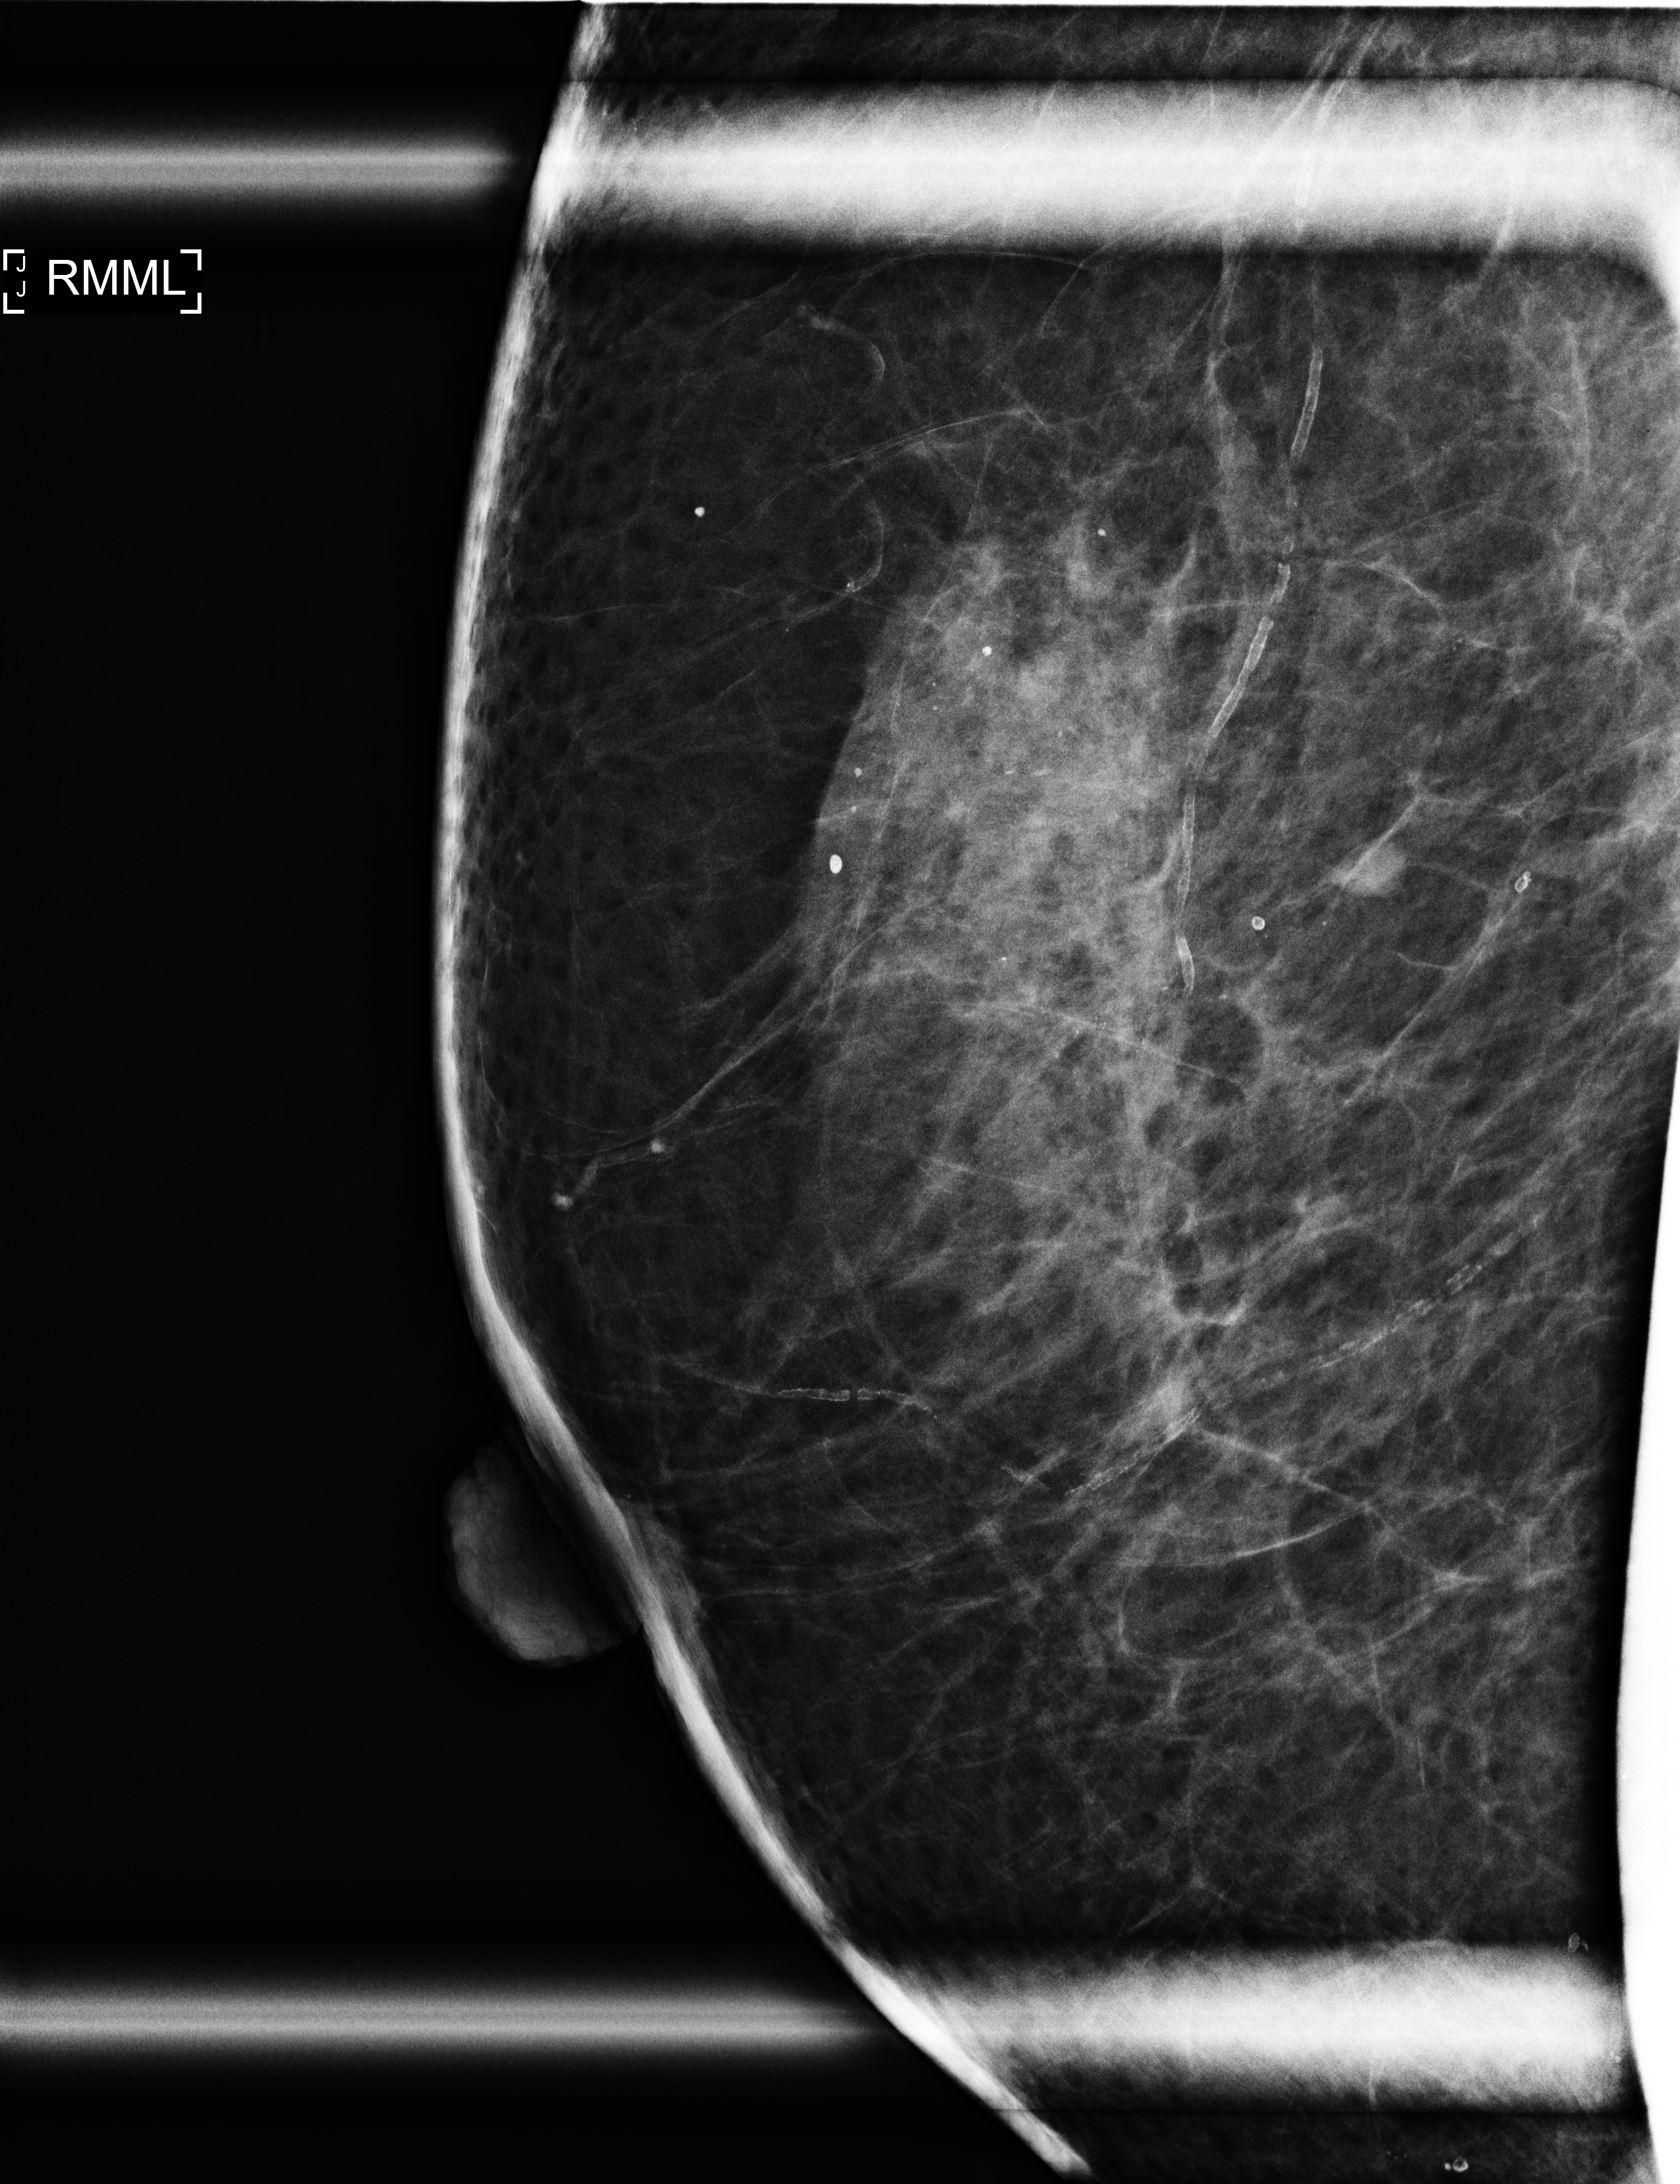
Additional (diagnostic) view; compressed breast thickness 63 mm; system: Selenia Dimensions. Patient: female, 68 years.
Image type: full-field digital mammogram. Breast: right. Projection: mediolateral (ML) view, magnification.